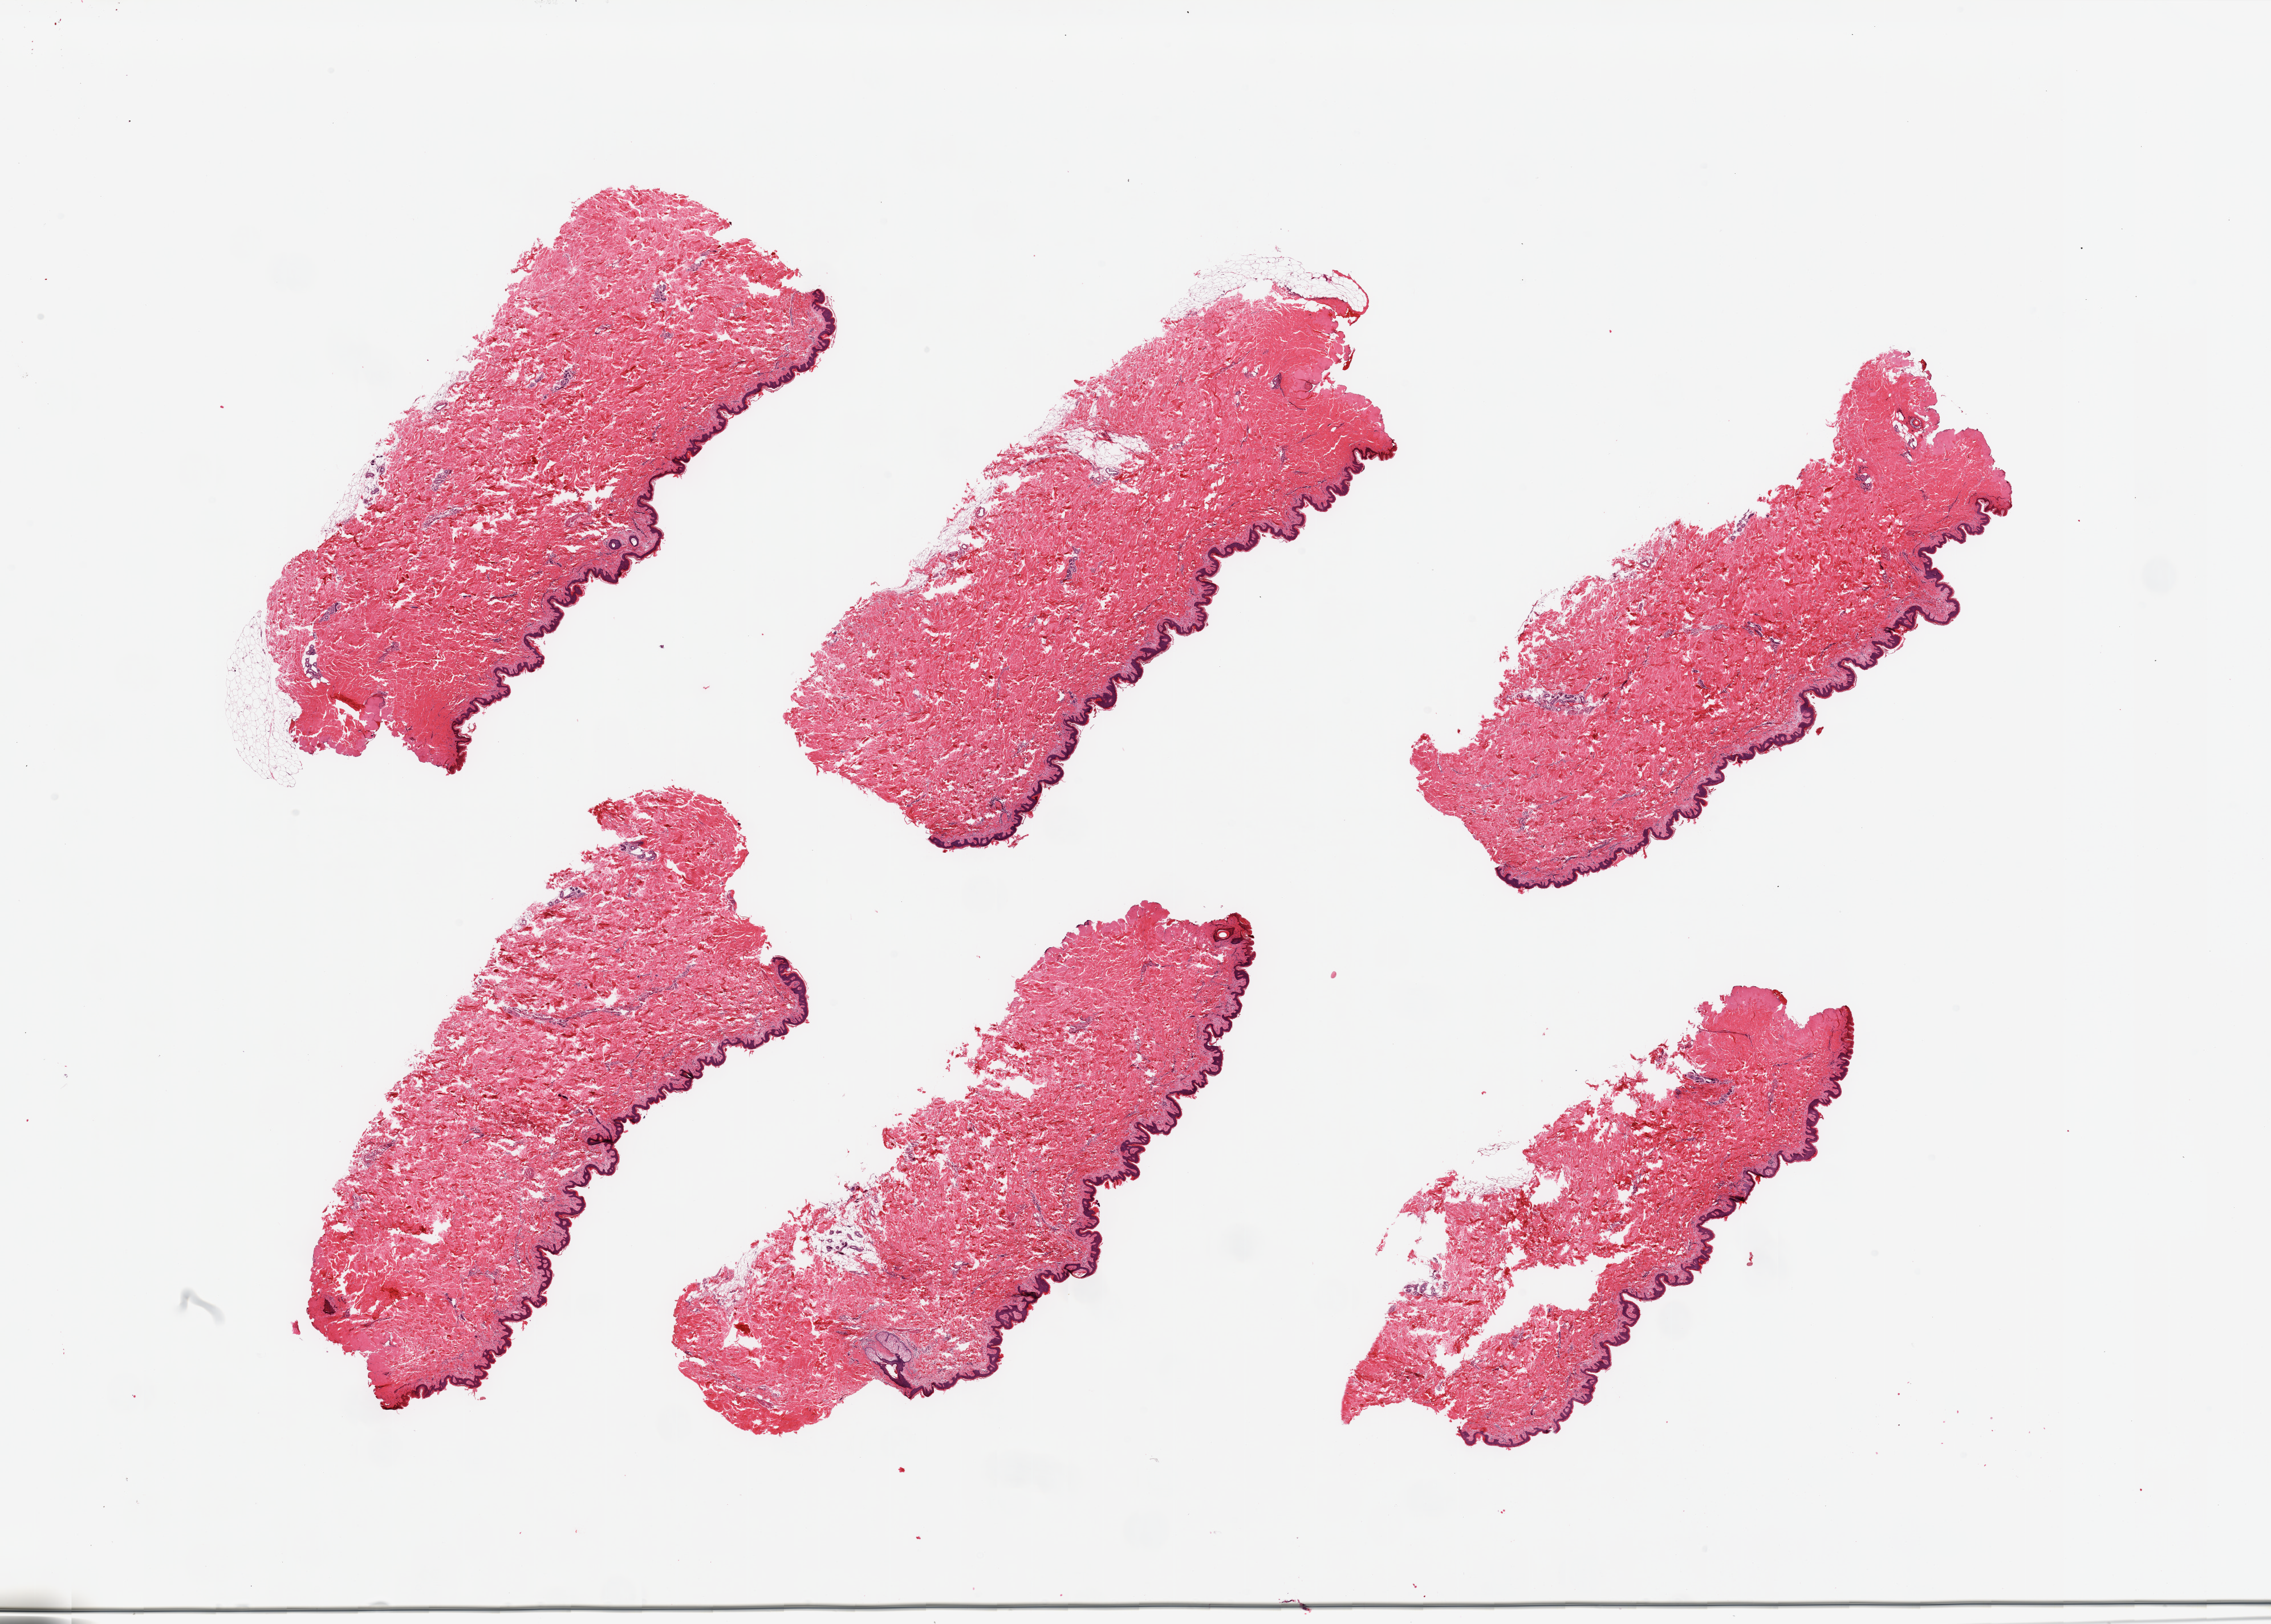
Haematoxylin and eosin whole-slide image, brightfield — shown as a low-resolution overview of the whole scanned area (about 31.5 x 22.5 mm, acquisition: 20x scan); PAXgene-fixed paraffin-embedded (PFPE) section; section of skin of suprapubic region (target tissue); tissue donor sample. Donor sex: male.
• review note (as recorded): 6 pieces; well trimmed, hairless; <5% dermal fat